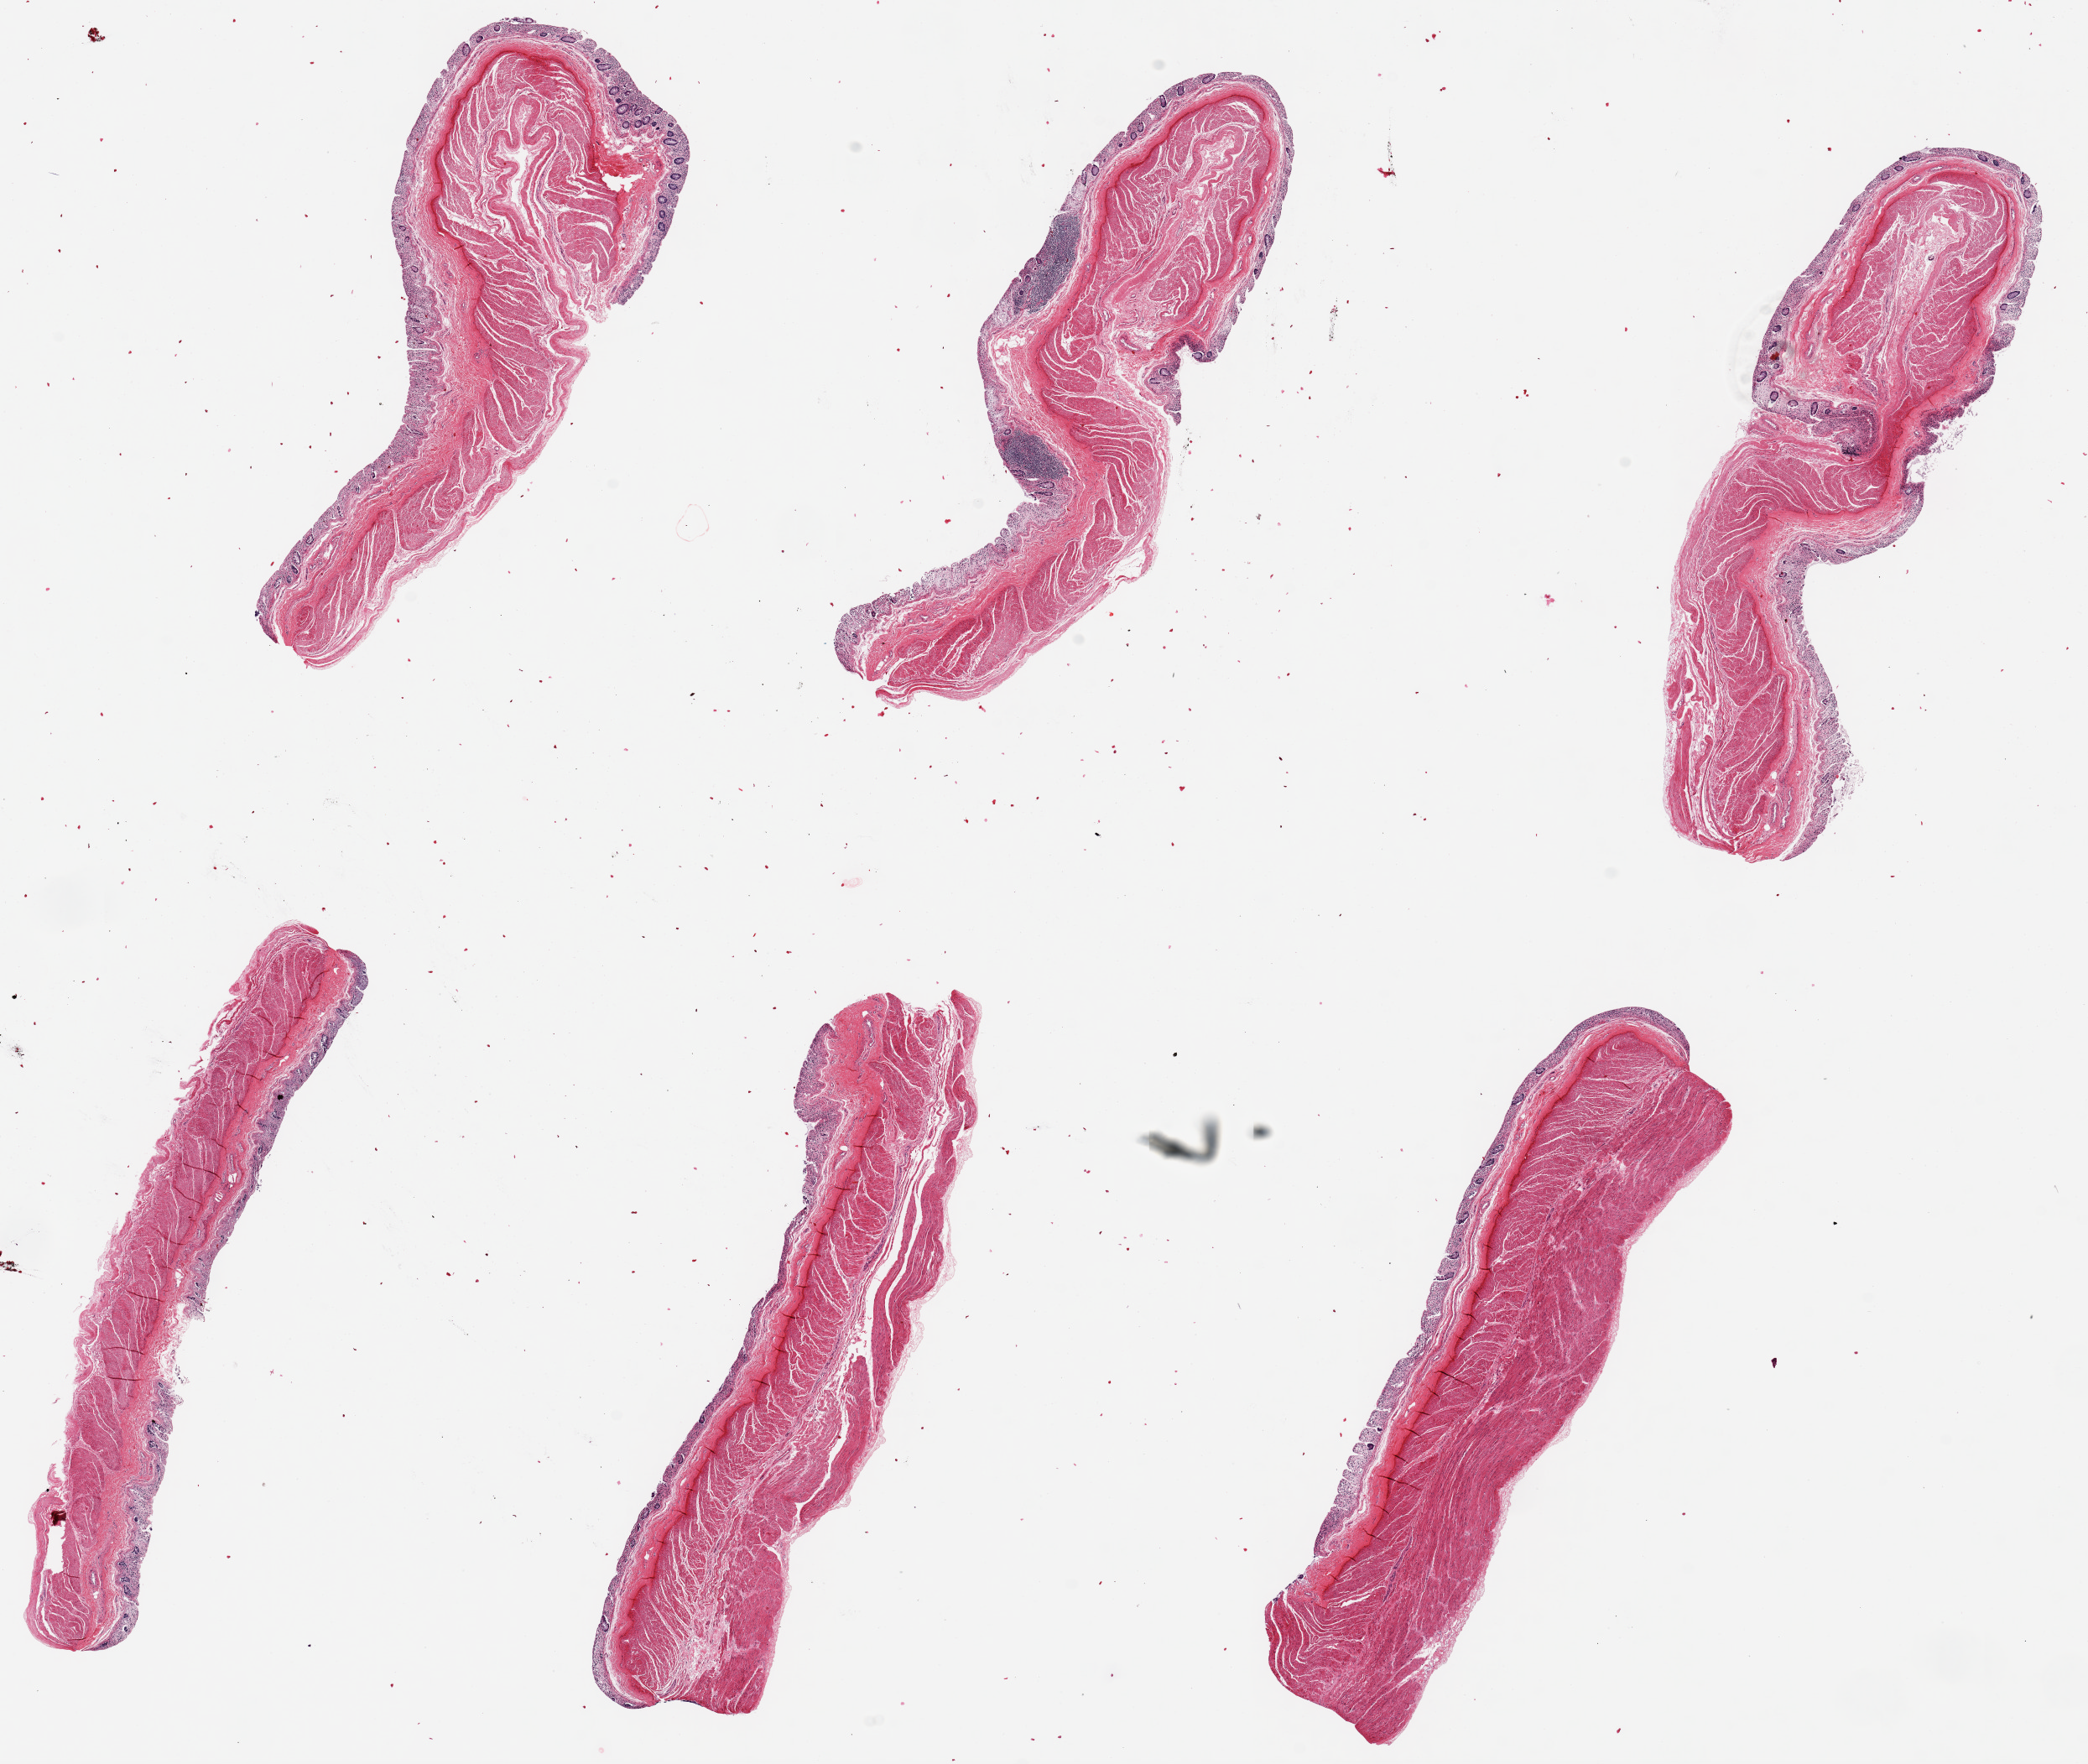
Haematoxylin and eosin whole-slide image, a low-resolution overview of the entire scanned area, about 19.7 x 16.6 mm. PAXgene-fixed paraffin-embedded (PFPE) section. Sampled site (target tissue): sigmoid colon. Tissue donor sample. Donor: male.
* pathologist's review note for this sample: 6 pieces ~7x2mm, ~90% muscularis